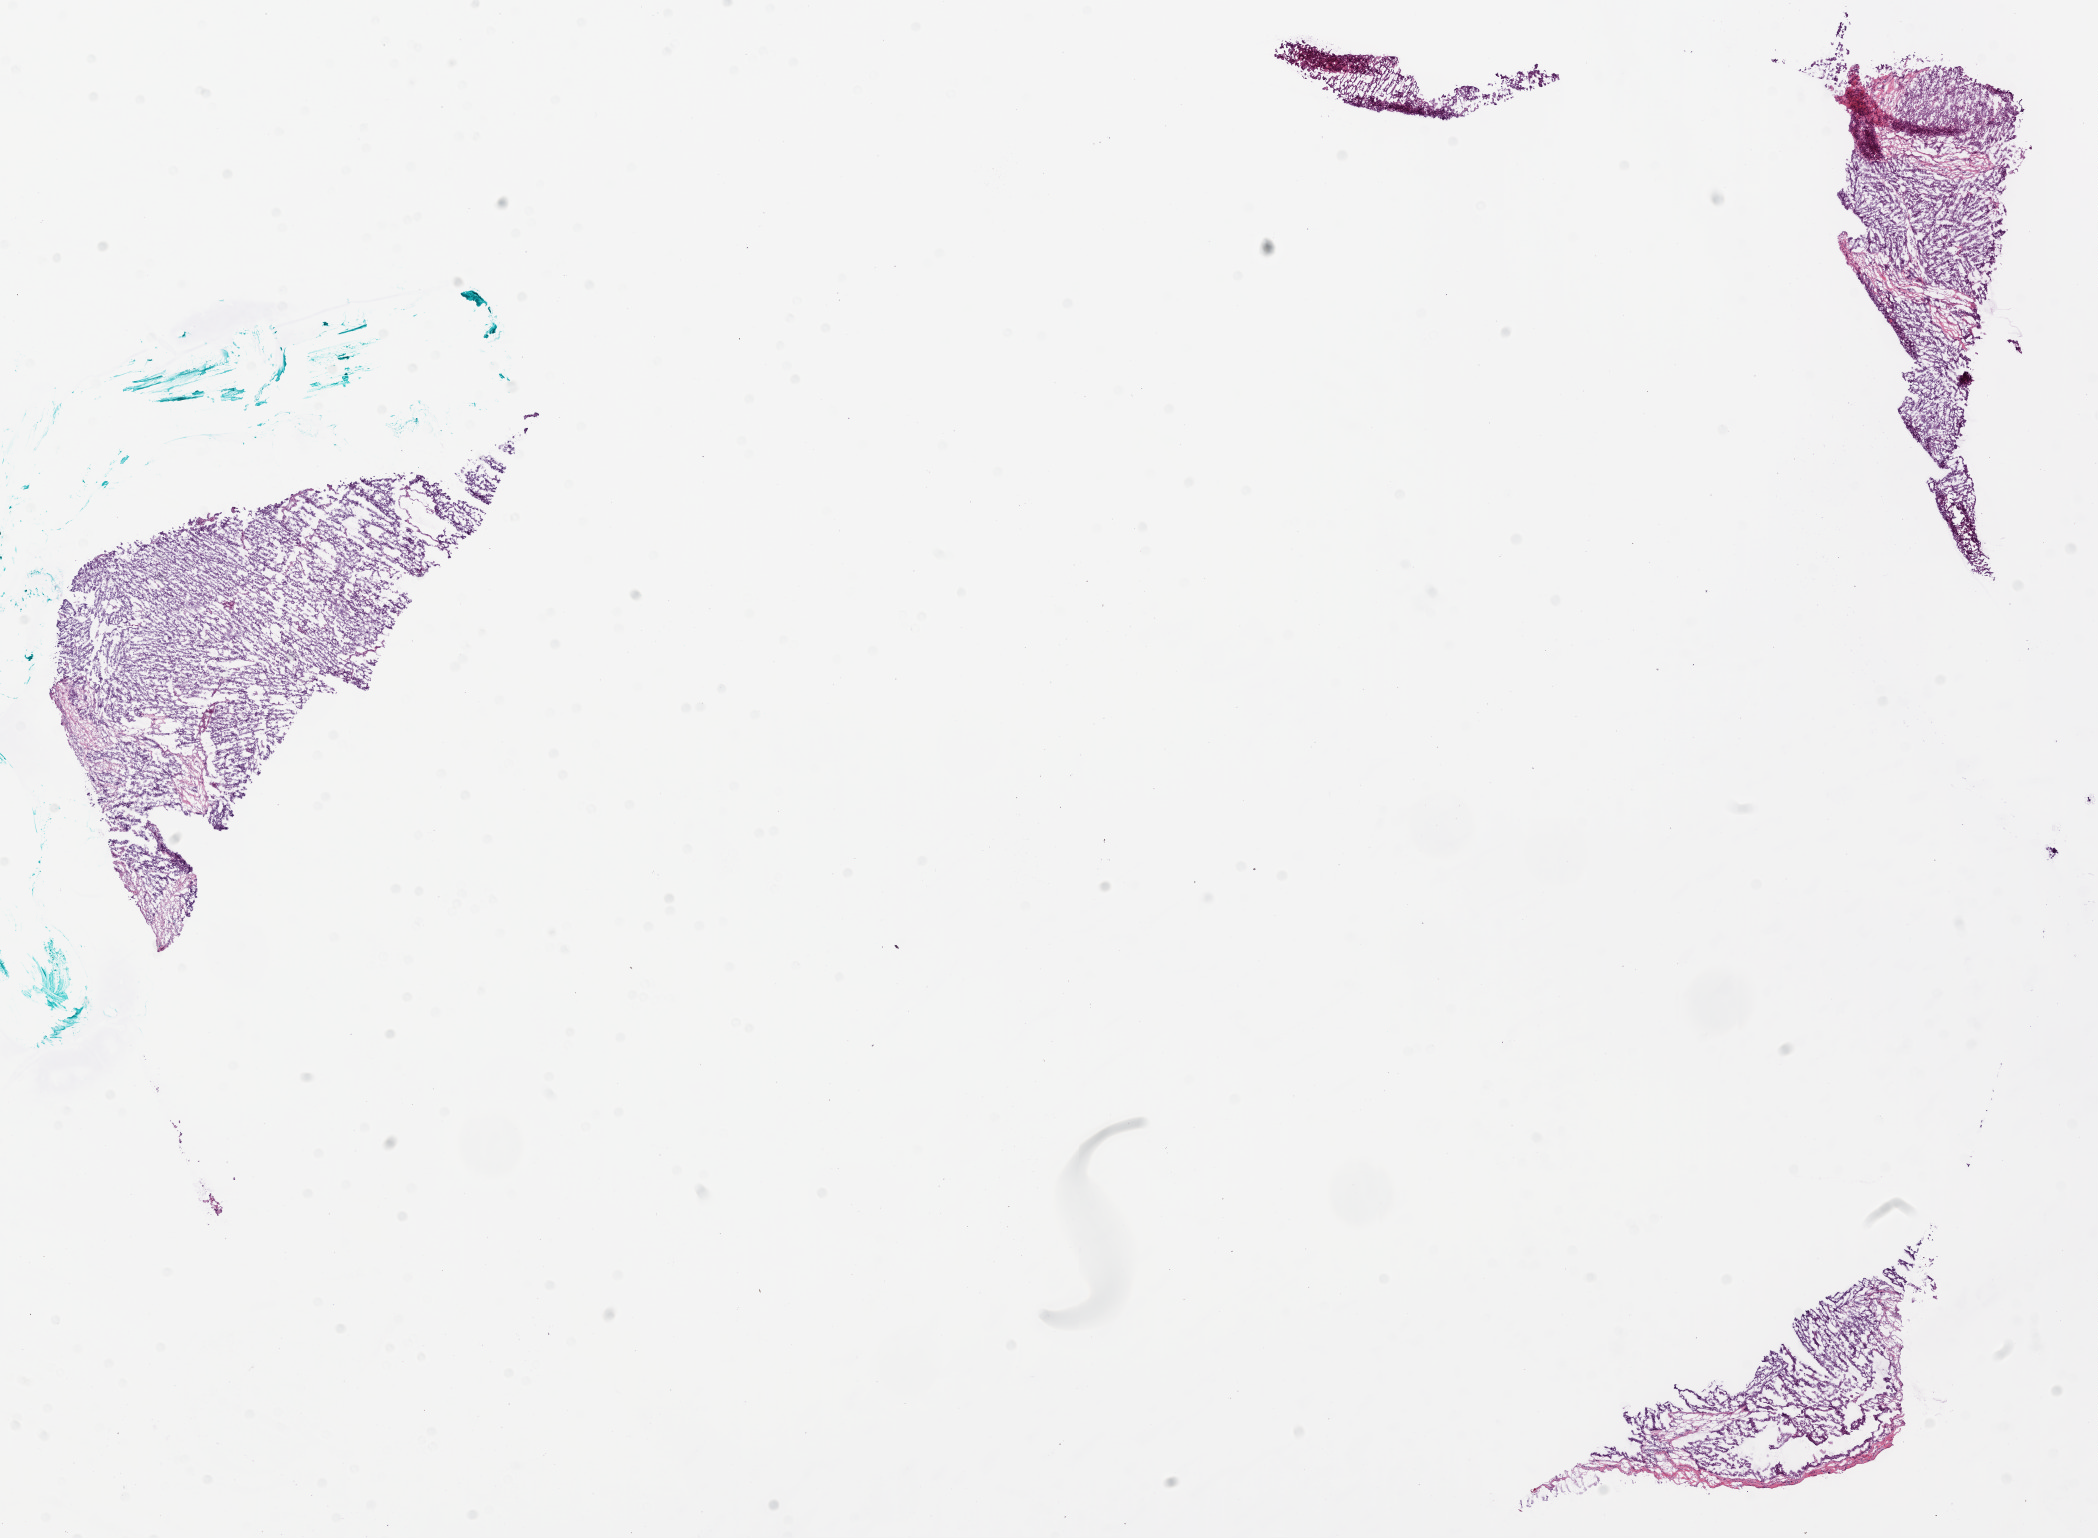
H&E whole-slide image, a low-resolution overview of the entire scanned area, about 16.9 x 12.4 mm (slide scanned at 20x); frozen section; primary tumour sample from the ovary. Patient: female, age at initial diagnosis 62 years. Histologic grade: G3 (poorly differentiated). Pathologist review of this section (percent, as recorded): tumour cells 79%, tumour nuclei 80%, normal cells 20%, necrosis 1%.
Laterality: bilateral. FIGO stage: IV. Diagnosis: Serous cystadenocarcinoma, NOS.